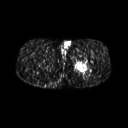
FDG PET of an extremity soft-tissue mass (from a PET/CT study), one axial slice; position 253 of 267 along the scan axis; 3.27 mm slice thickness; 128 × 128 image matrix, field of view 500 × 500 mm. Male patient, age 27 years. From the clinical record (not read from this slice): histological type: extraskeletal osteosarcoma; grade: high; site of the primary tumour: left adductur.
Outlined on this slice (expert contour drawn on MRI and transferred to this co-registered scan by the dataset authors):
- gross tumour volume (mass): box from (x=71, y=55) to (x=95, y=75) px